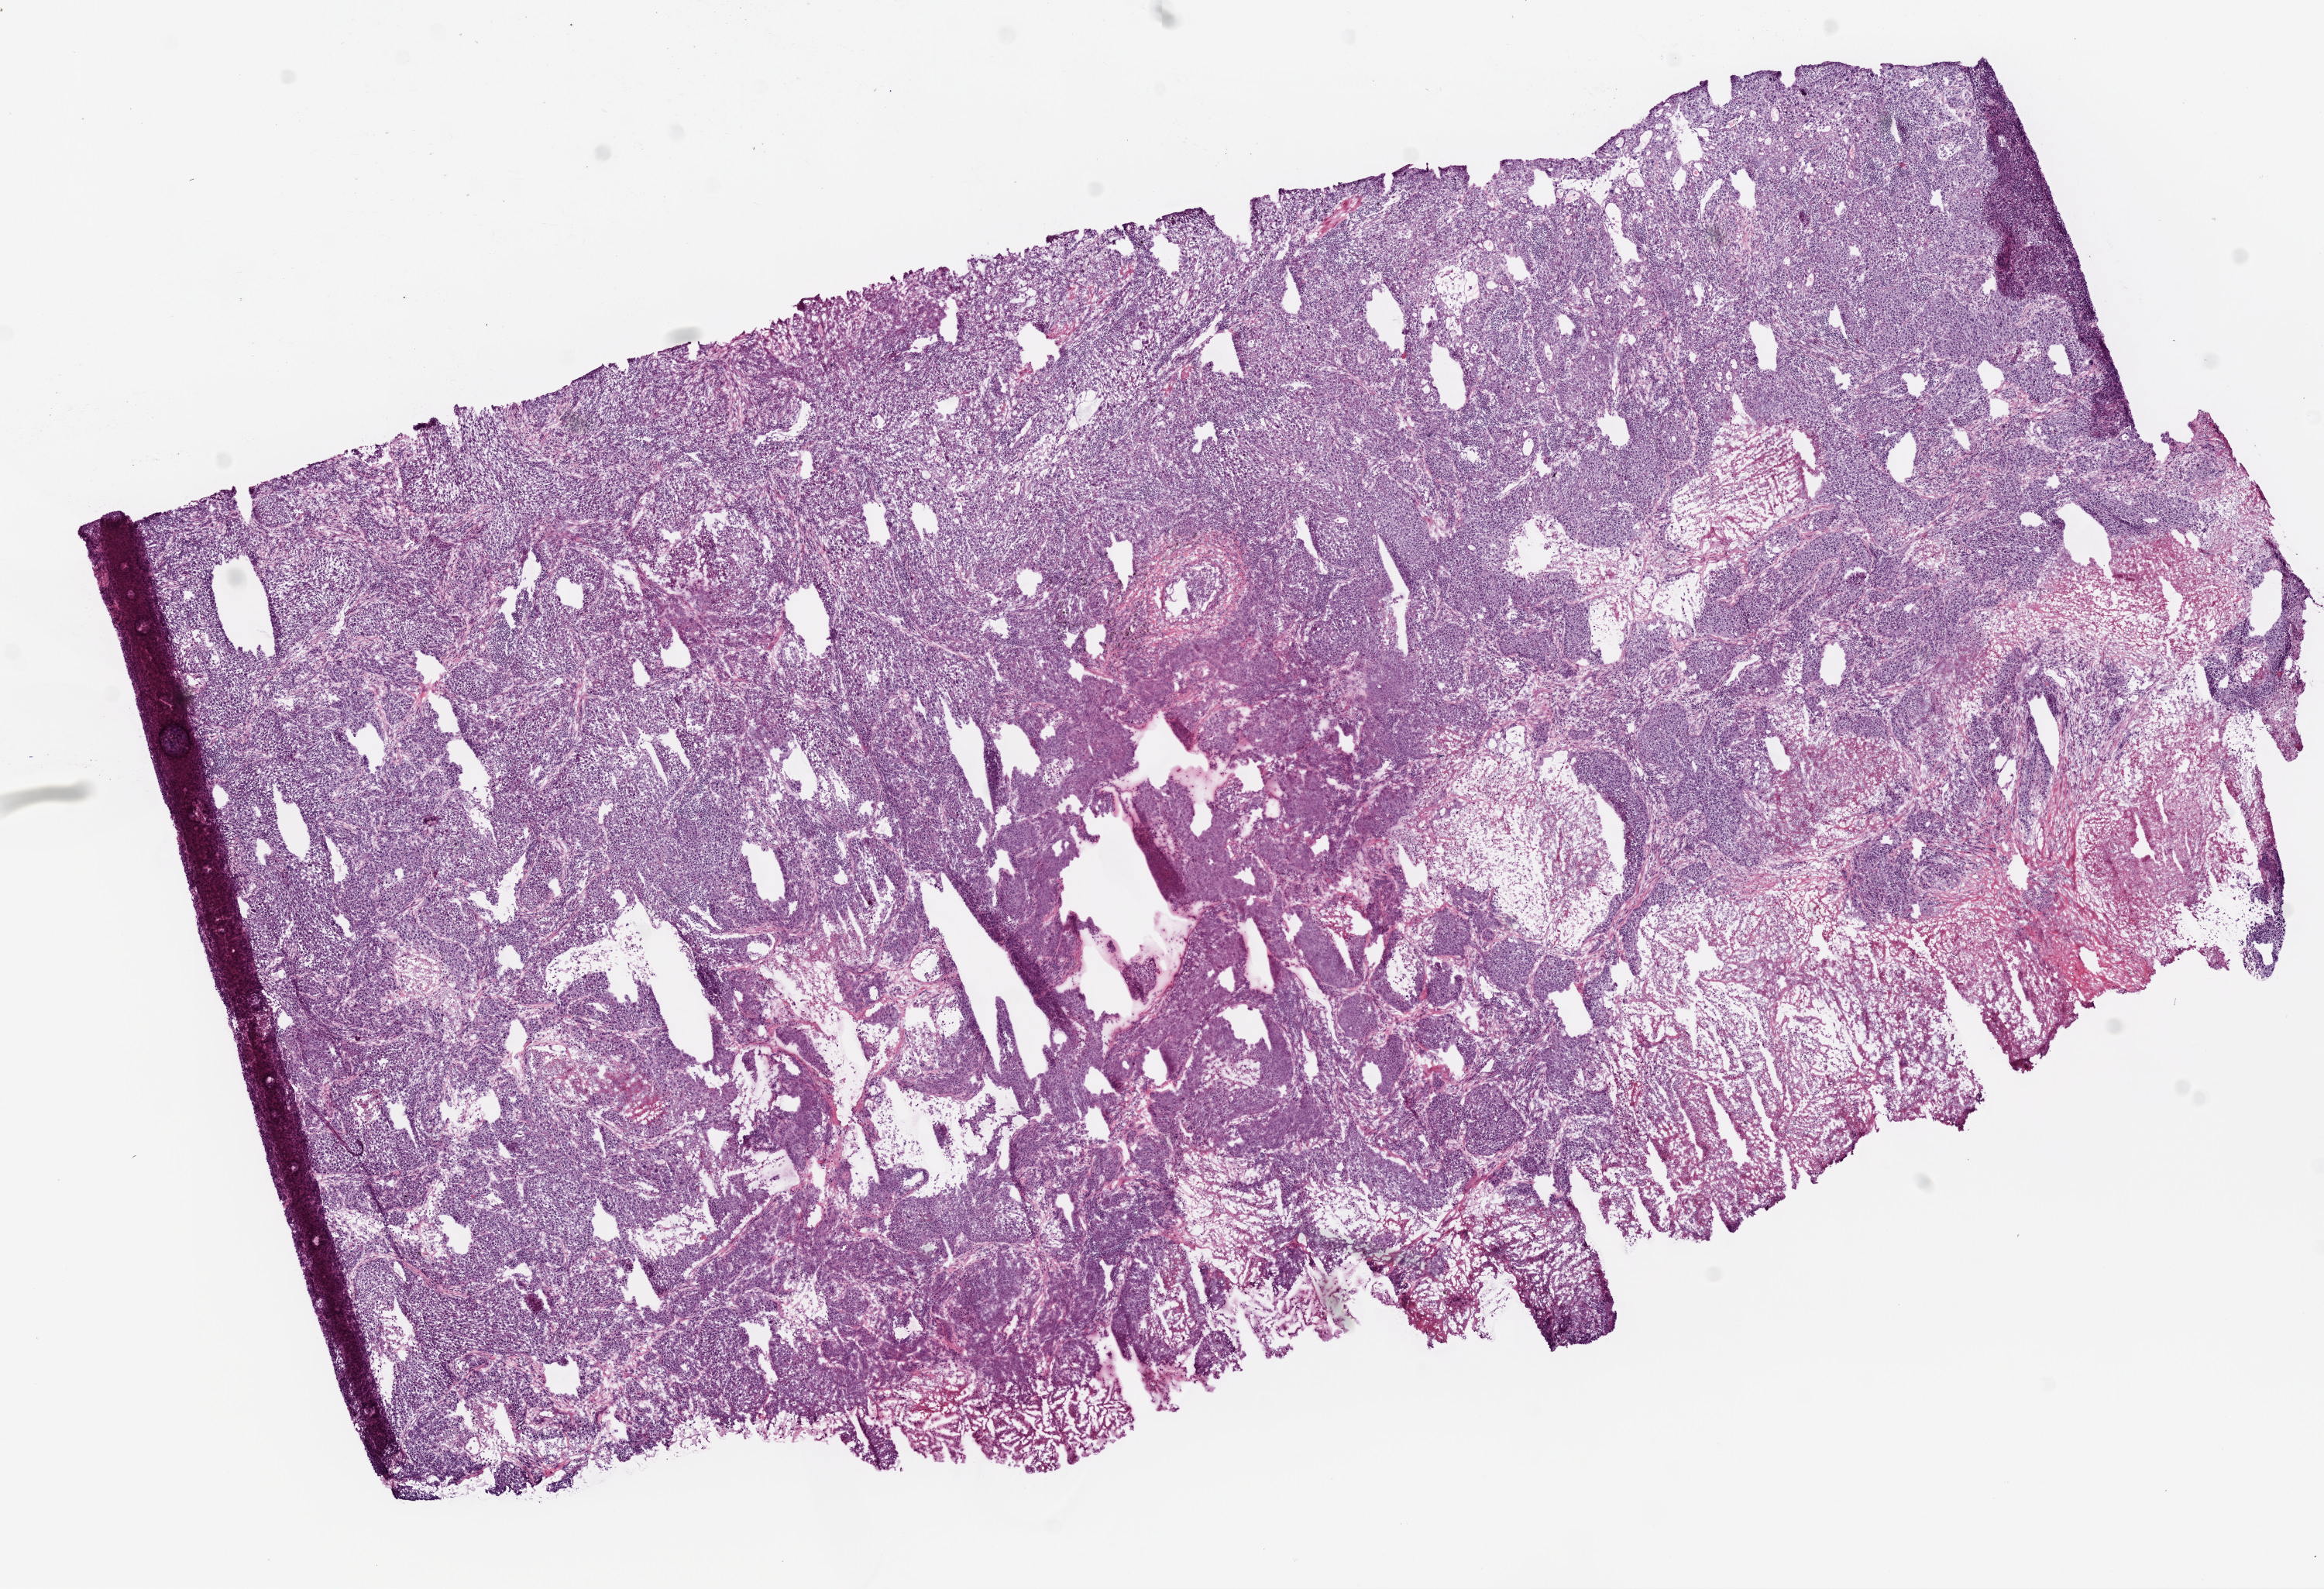
Digitized Hematoxylin and eosin (H&E) stained tissue section (whole slide), whole scanned area (about 12.0 x 8.2 mm, slide scanned at 20x) shown as a low-resolution overview; frozen section from the top of the tissue portion; sample: primary tumour, lung. Male patient; age at initial diagnosis 65 years. Slide review estimates, as recorded: tumour cells 75%, tumour nuclei 70%, normal cells 0%, stromal cells 5%, necrosis 20%. Infiltration values recorded for this section: lymphocyte infiltration 22%, monocyte infiltration 0%, neutrophil infiltration 0%.
AJCC pathologic stage: IB (6th edition). Laterality: left. Histologic diagnosis: Squamous cell carcinoma, NOS (upper lobe, lung).